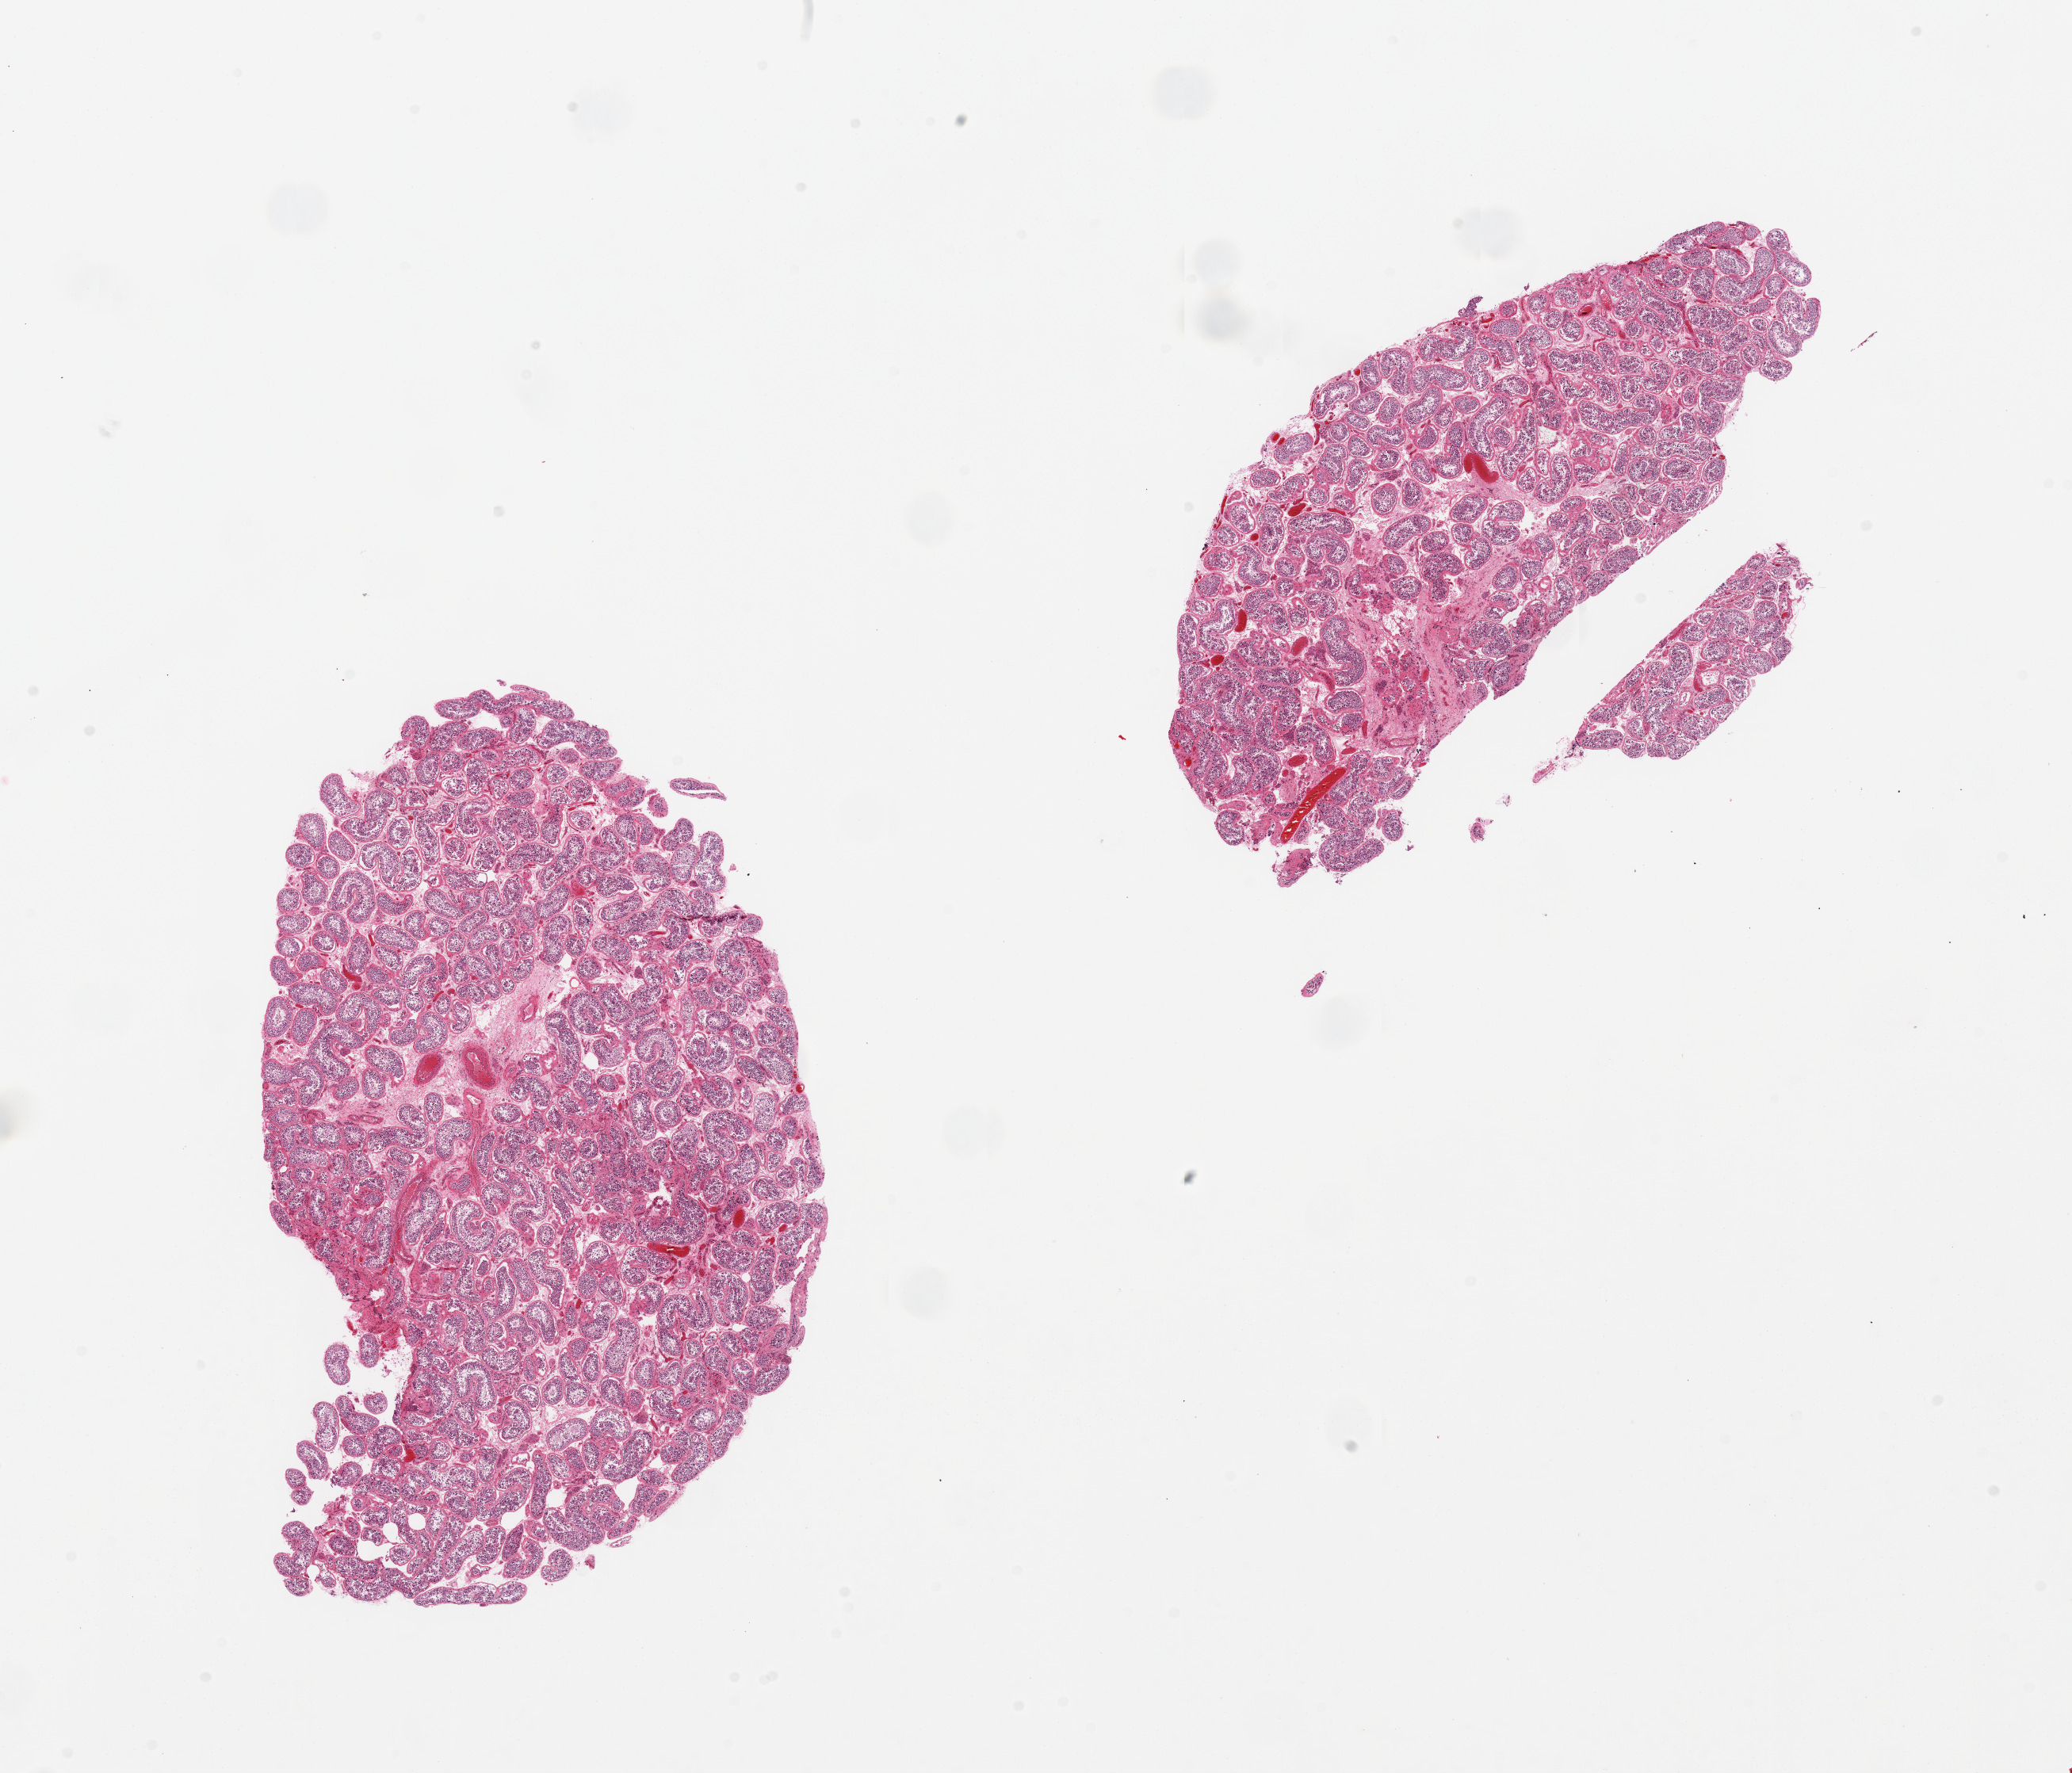
Hematoxylin and eosin (H&E) whole-slide image — low-resolution overview of the scanned area, about 20.7 x 17.7 mm (acquisition: 20x scan); PAXgene-fixed paraffin-embedded (PFPE) section; section of testis (target tissue); donor tissue sample.
Pathologist's review note for this sample: 2 pieces, increased peritubular fibrosis, spermatogenesis present.